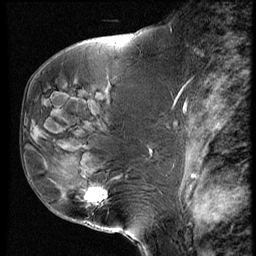
Breast MRI (dynamic contrast-enhanced), one sagittal slice. Position 29 of 60 along the scan axis. Dynamic contrast-enhanced series, image 2 of 4 at this slice position (ordered by acquisition). 1.5 T. TE 4.2 ms, TR 9 ms. 2.5 mm slice thickness. 256 × 256 image matrix, field of view 180 × 180 mm. Patient: female, 50 years. From the clinical record (not read from this slice): setting: breast cancer imaged before/during neoadjuvant chemotherapy; receptor status: HR-positive, HER2-negative.
Structures marked on this image (semi-automatically segmented with operator editing):
- analysis volume of interest (the breast-tissue region the enhancement analysis was run in; not a lesion): box from (x=48, y=109) to (x=135, y=230) px
- tumour enhancement mask (voxels above the 140 % enhancement threshold inside the analysis volume of interest): (x=84, y=189)–(x=107, y=203)